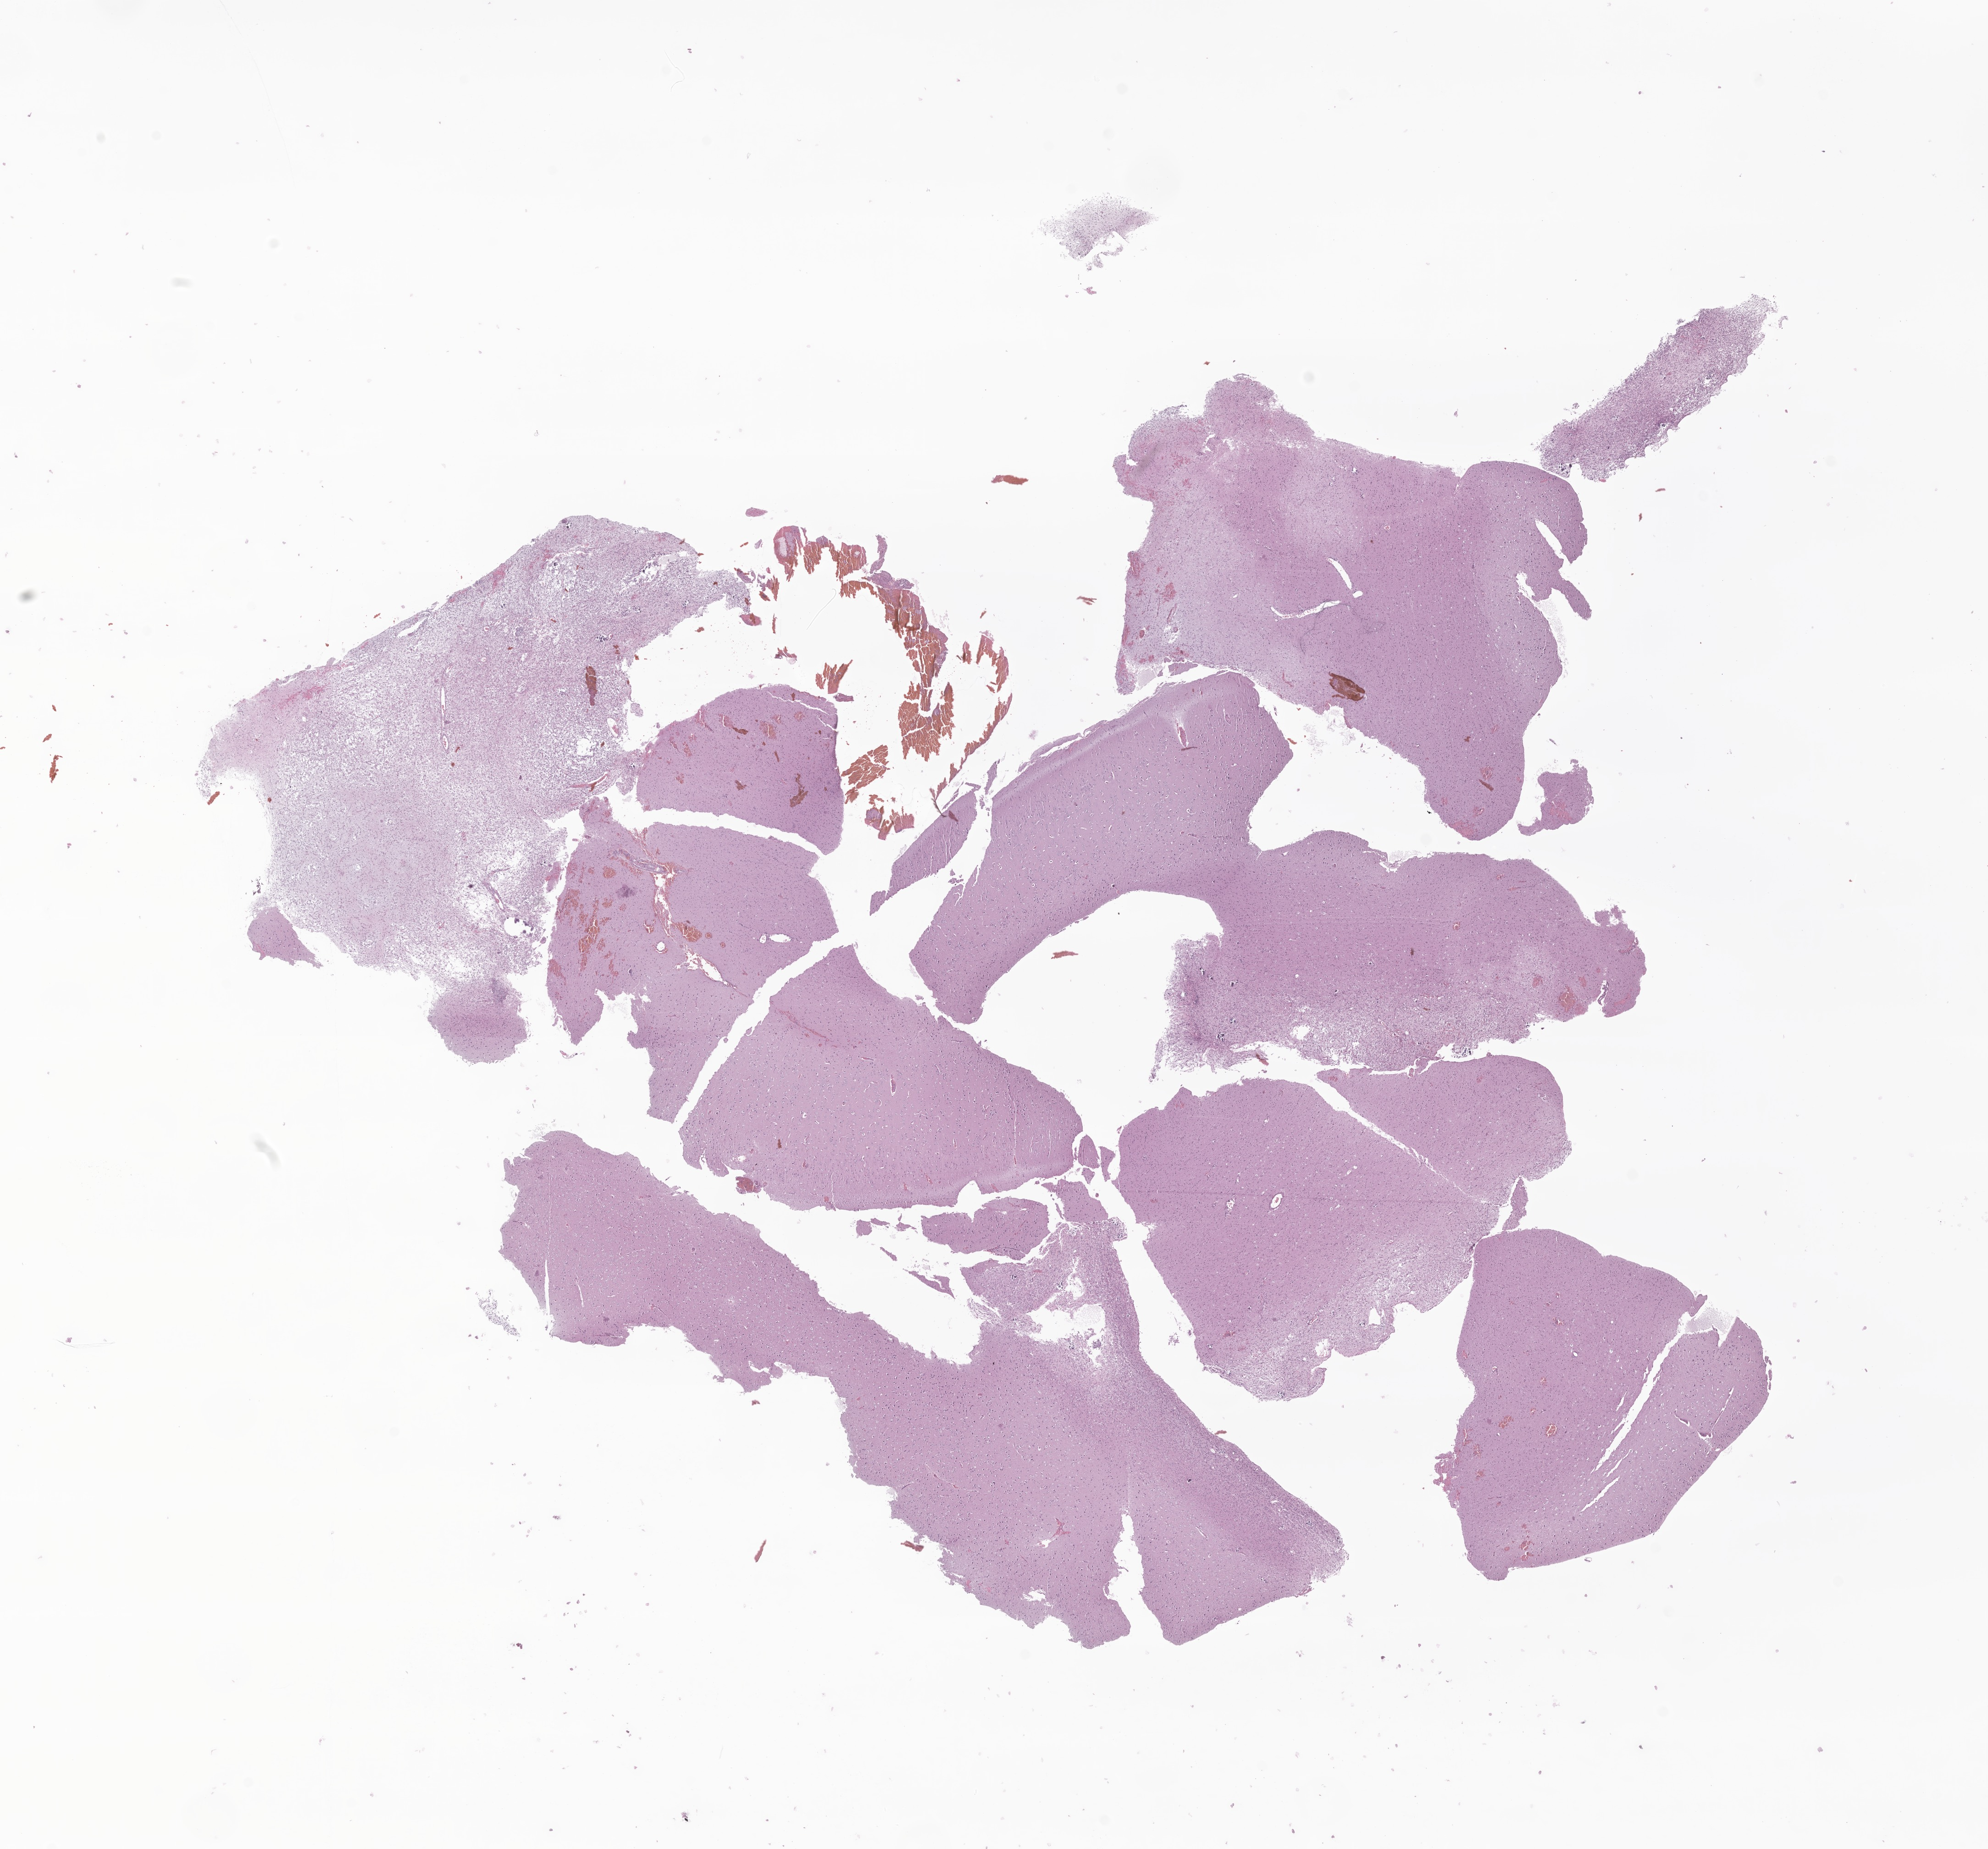
H&E whole-slide image of tumor tissue from the temporal lobe, a low-resolution overview of the entire scanned area, about 18.3 x 17.0 mm; FFPE section. Patient female; age 37 months (3 years 1 month).
Recorded diagnosis: Oligoastrocytoma, NOS.